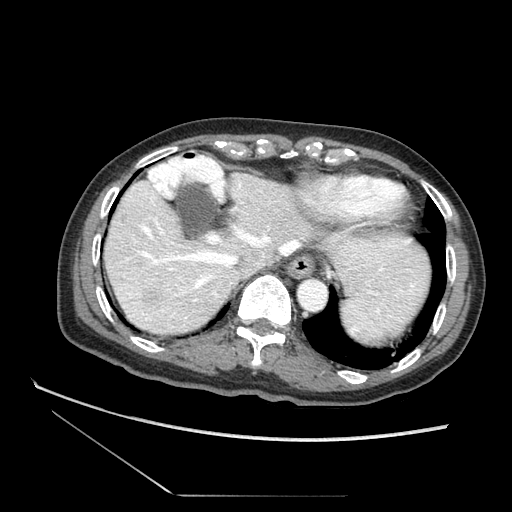
Contrast-enhanced abdominal CT (liver protocol), one axial slice. Reconstruction kernel STANDARD. 120 kVp. Soft-tissue window (W 400 / L 40 HU). 512 × 512 image matrix, field of view 360 × 360 mm. Case-level facts recorded for this patient, not image findings: diagnosis: hepatocellular carcinoma (patient treated with transarterial chemoembolisation; whether this scan precedes or follows treatment is not stated here); TNM stage (as recorded): Stage-II; Child-Pugh class: A; tumour differentiation: moderately differentiated; tumour size: 3.8 cm.
Outlined on this slice (semi-automatically segmented with operator editing):
- abdominal aorta: bounding box [x1, y1, x2, y2] px = [300, 280, 329, 311]
- liver parenchyma outside the tumour (the mass and vessels are separate outlines, so this box may not span the whole liver): [98, 170, 438, 346]
- mass: [117, 271, 183, 315]
- liver vessels: [98, 239, 399, 328]